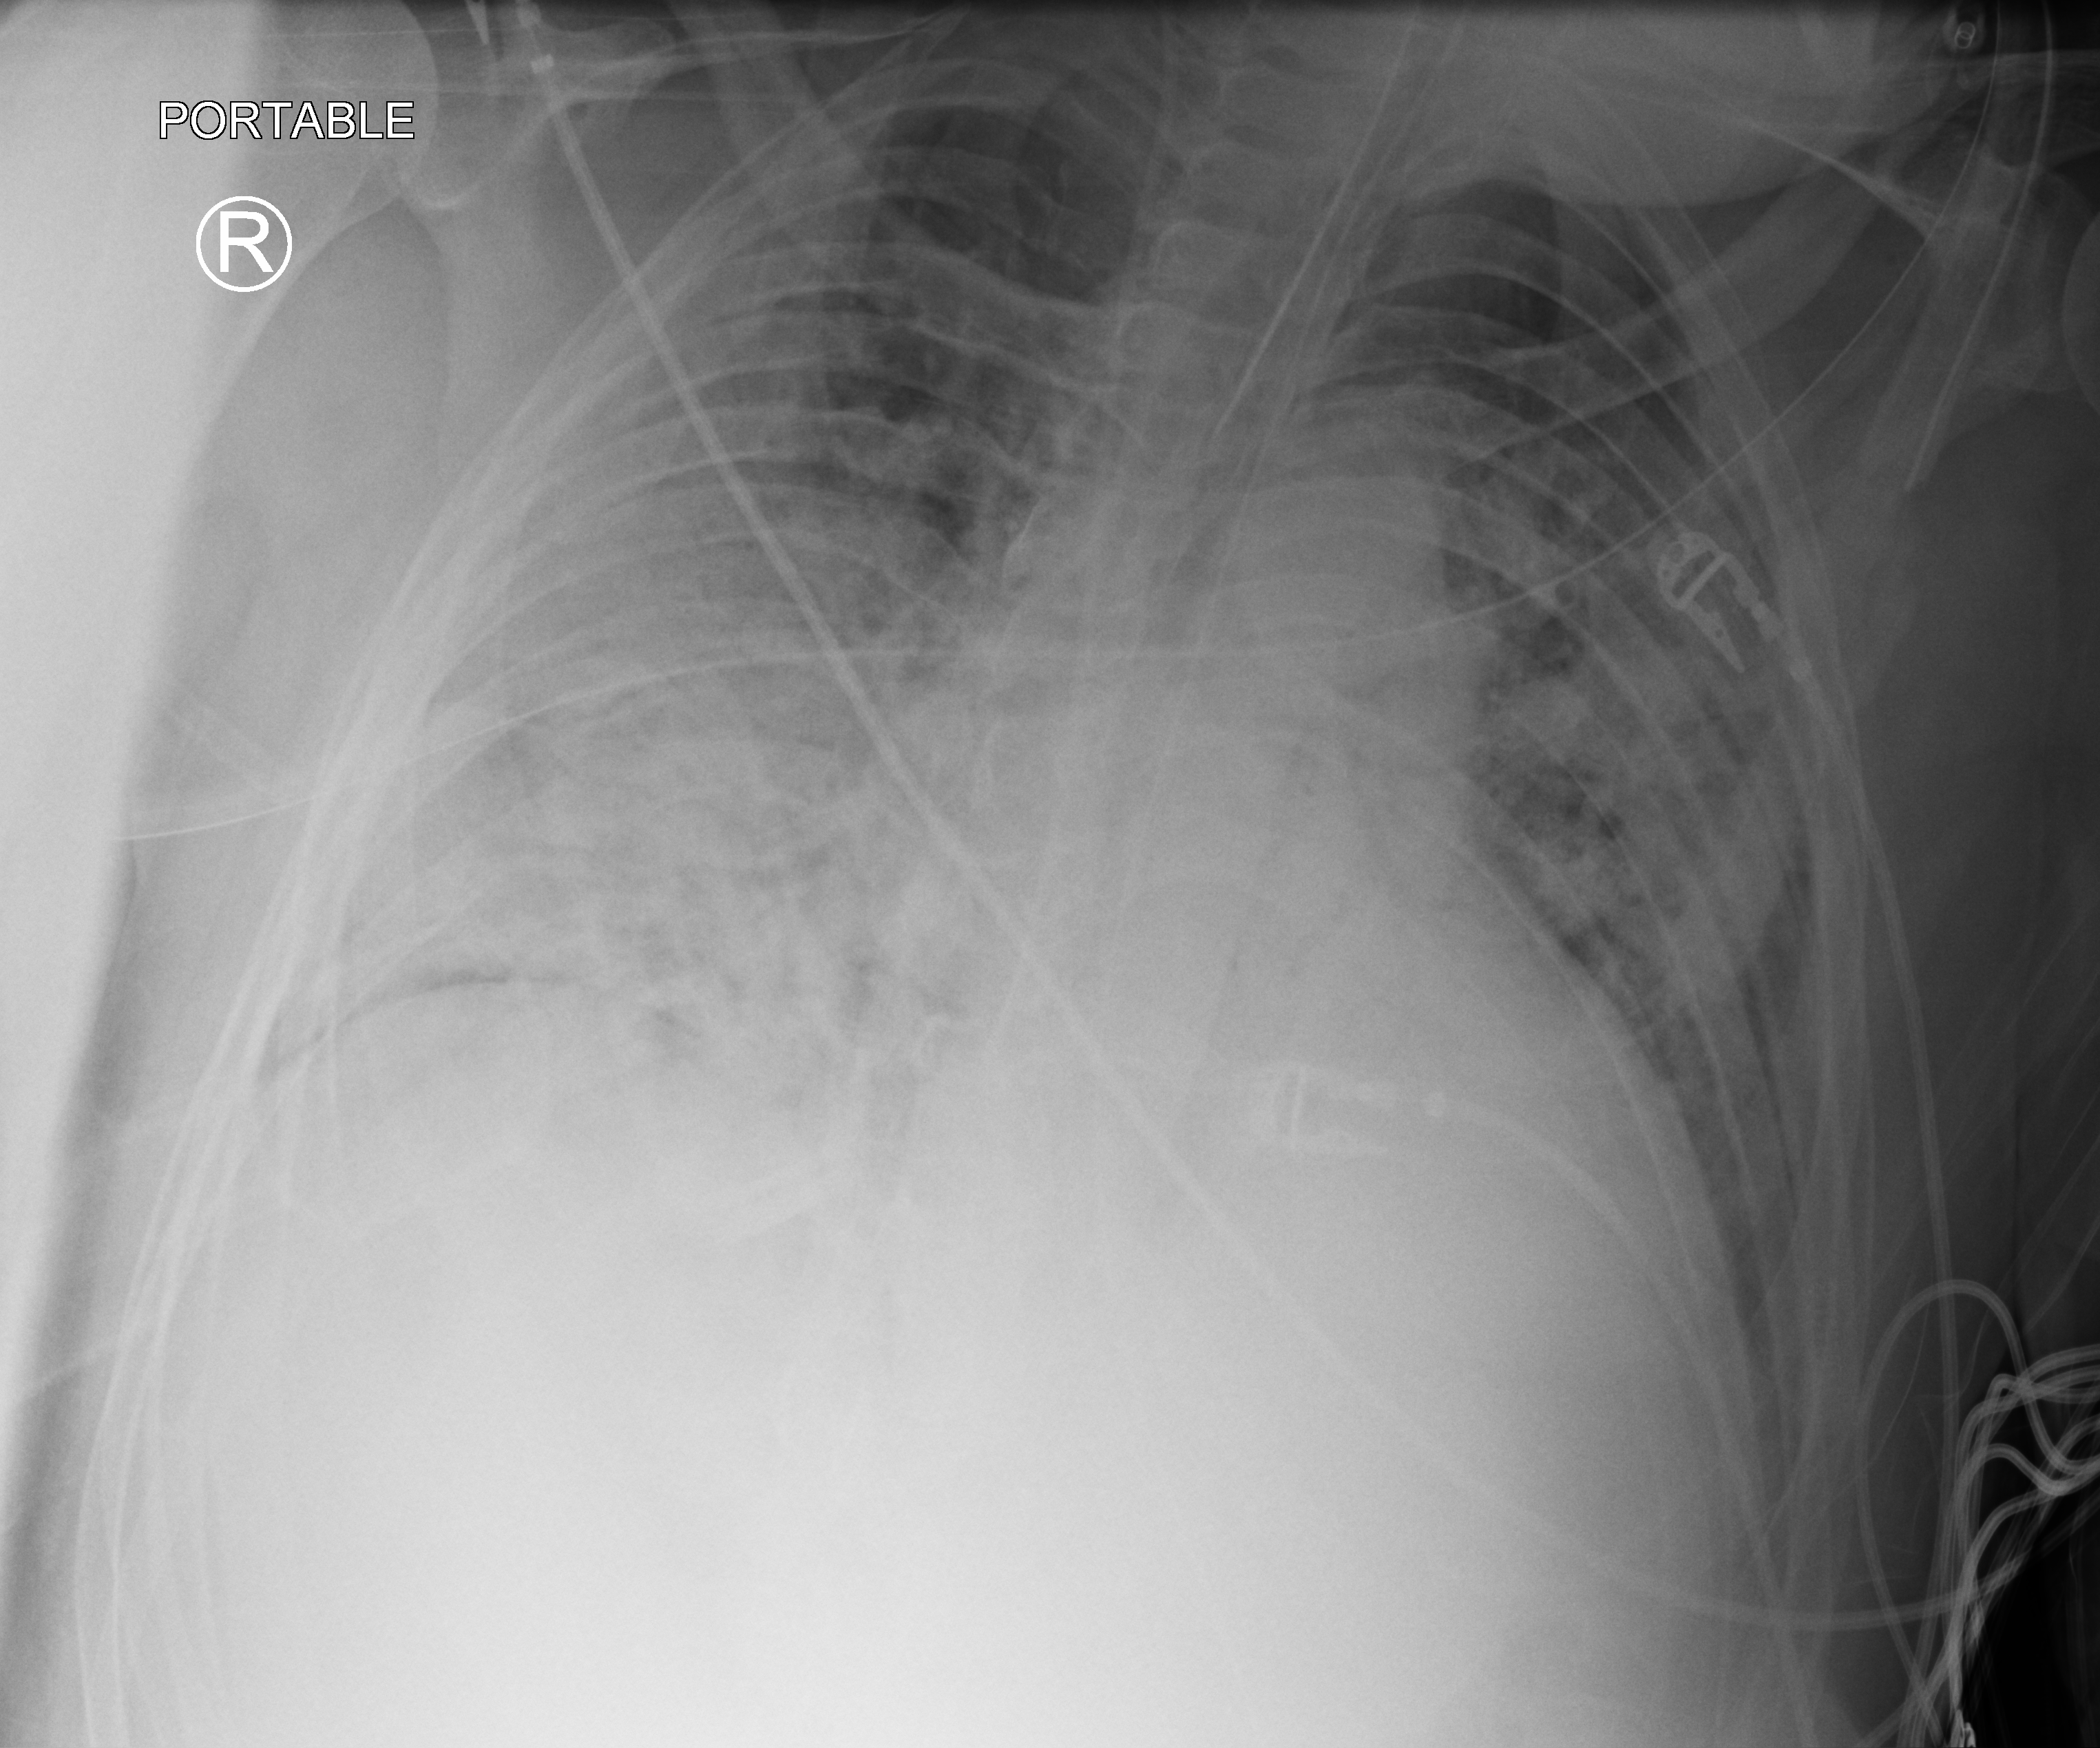
Bedside chest radiograph (computed radiography), anteroposterior (AP) projection. Male patient hospitalised with COVID-19, age 18–59 years.
Hospital-stay facts (about this admission, not read from this image; timing relative to this image not recorded):
- admitted to intensive care during this hospital stay: yes